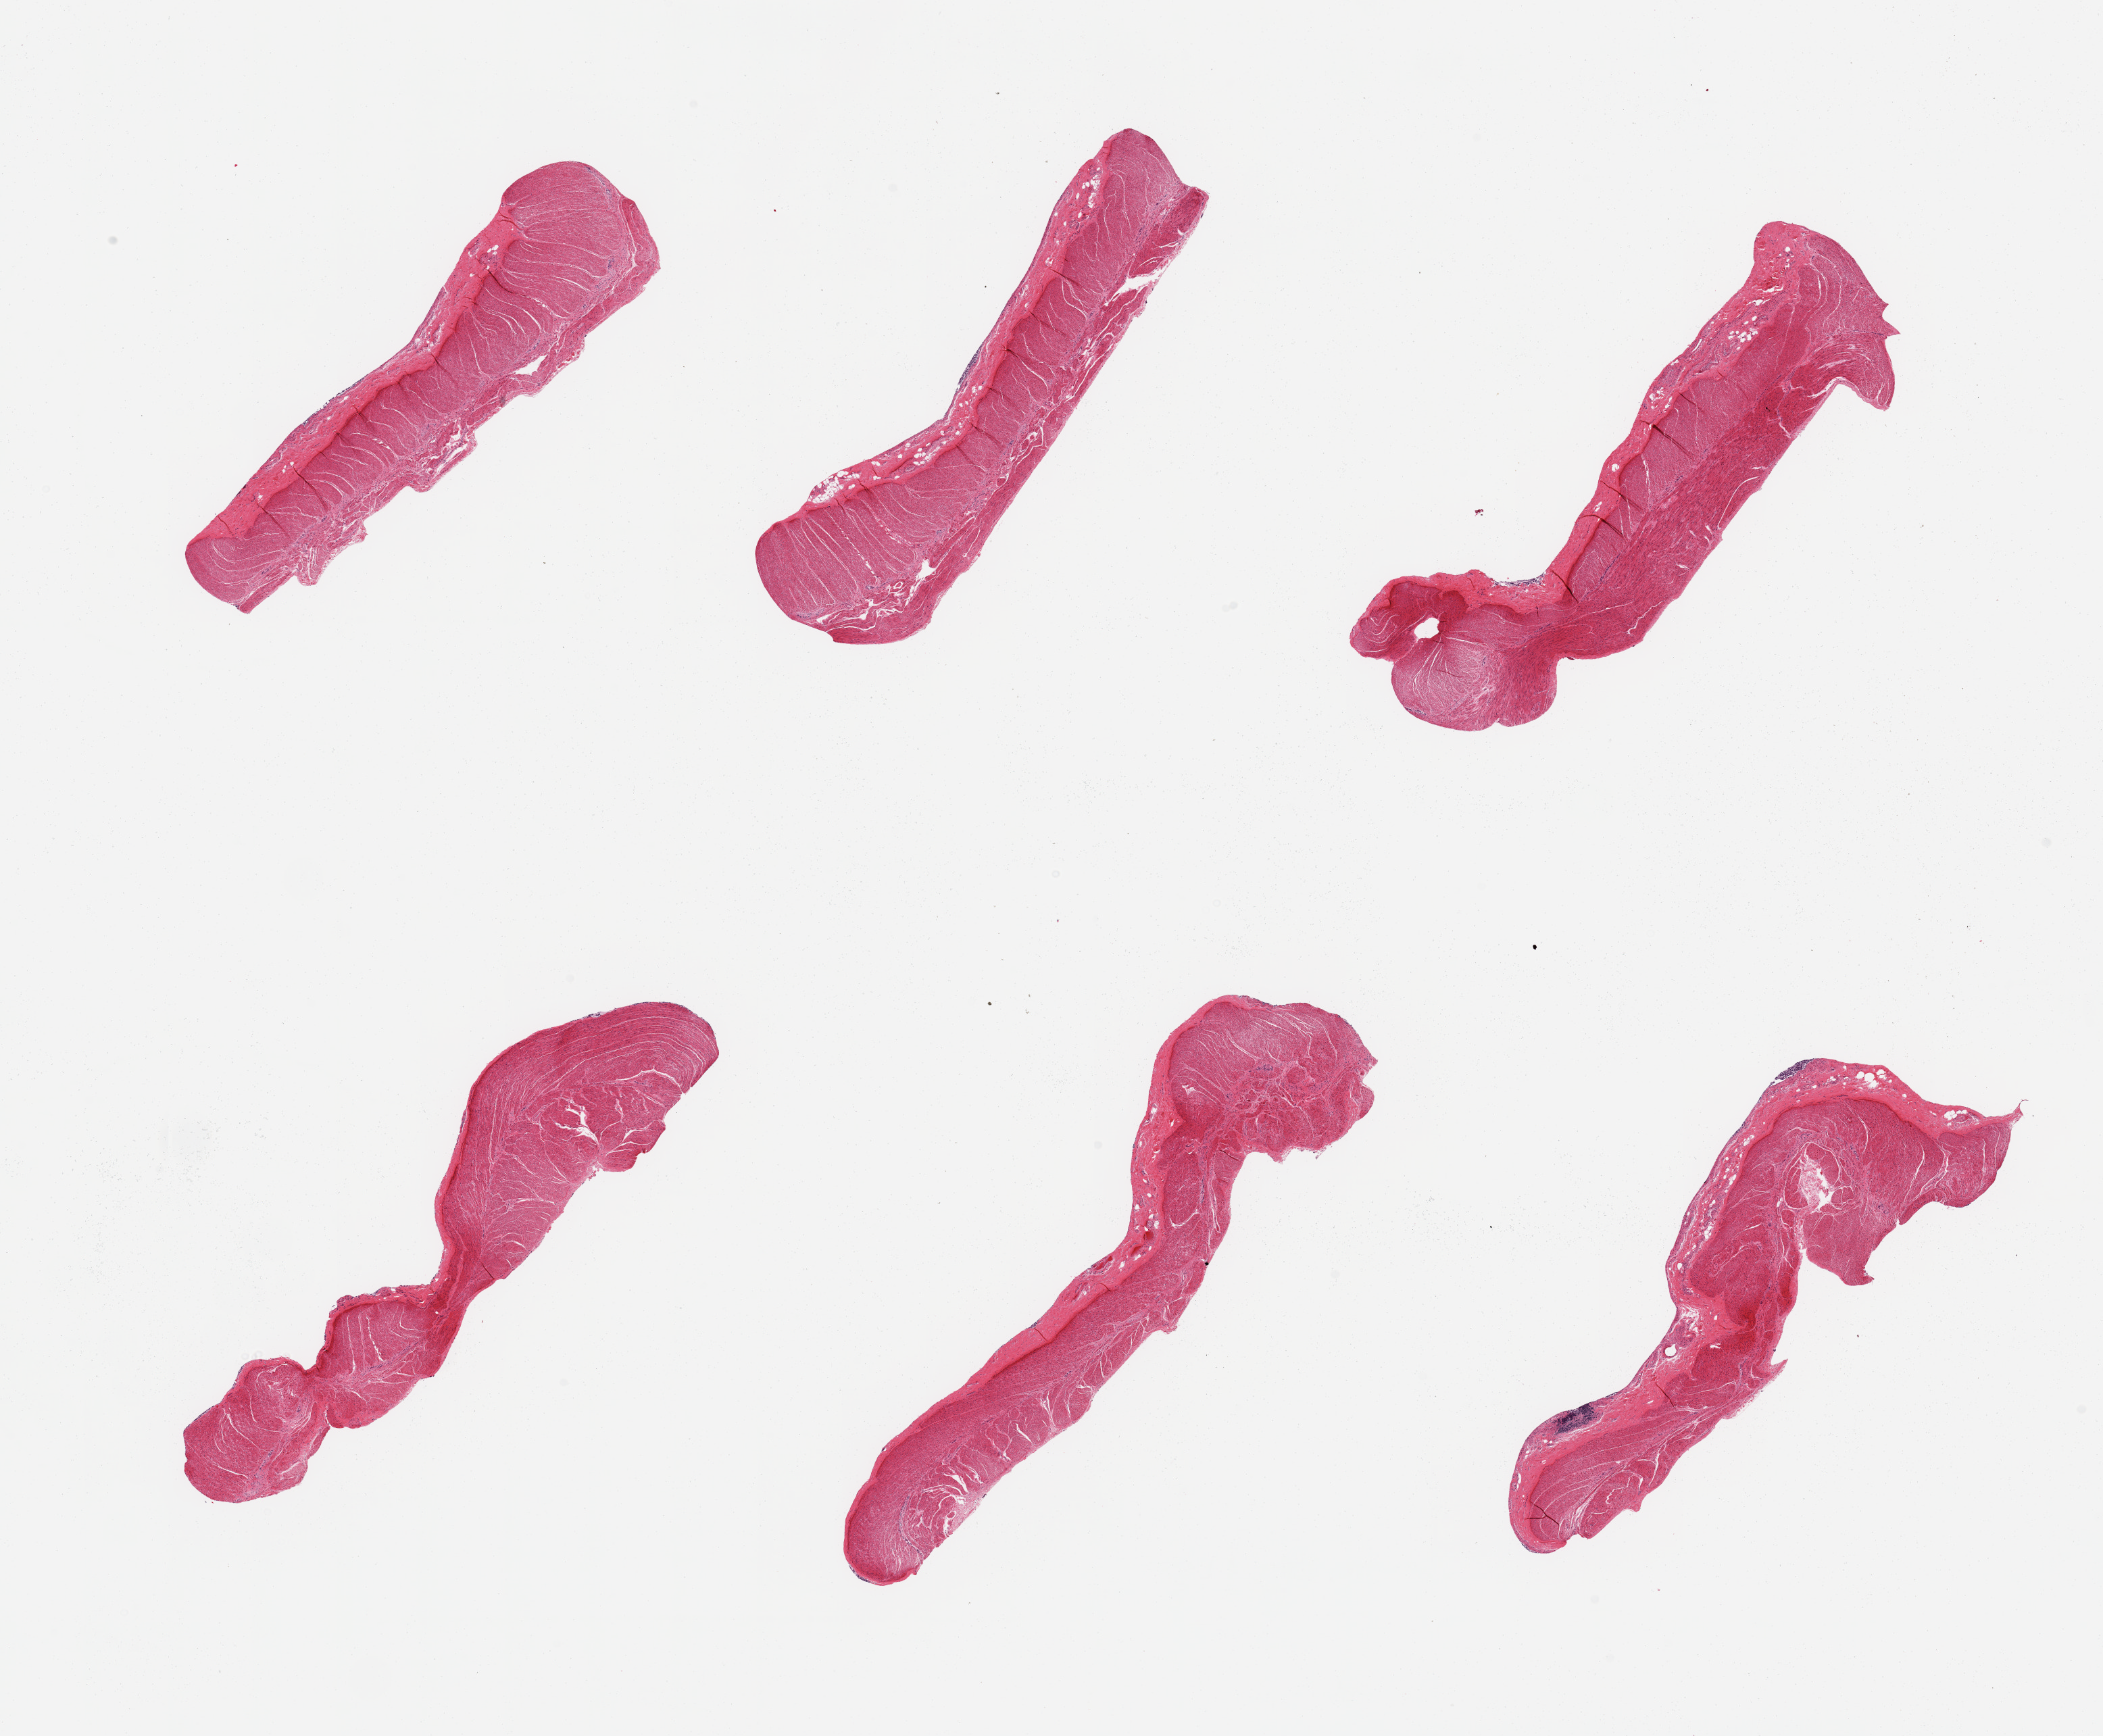
Digitized haematoxylin and eosin-stained section — whole scanned area (about 24.6 x 20.3 mm, from a 20x scan) shown as a low-resolution overview; PAXgene-fixed, paraffin-embedded tissue; section of sigmoid colon (target tissue); donor tissue sample. Donor sex: male.
Reviewer comment on this tissue sample: 6 pieces; fibrous submucosa up to 0.5 mm thick; 10-20% fibrous content.